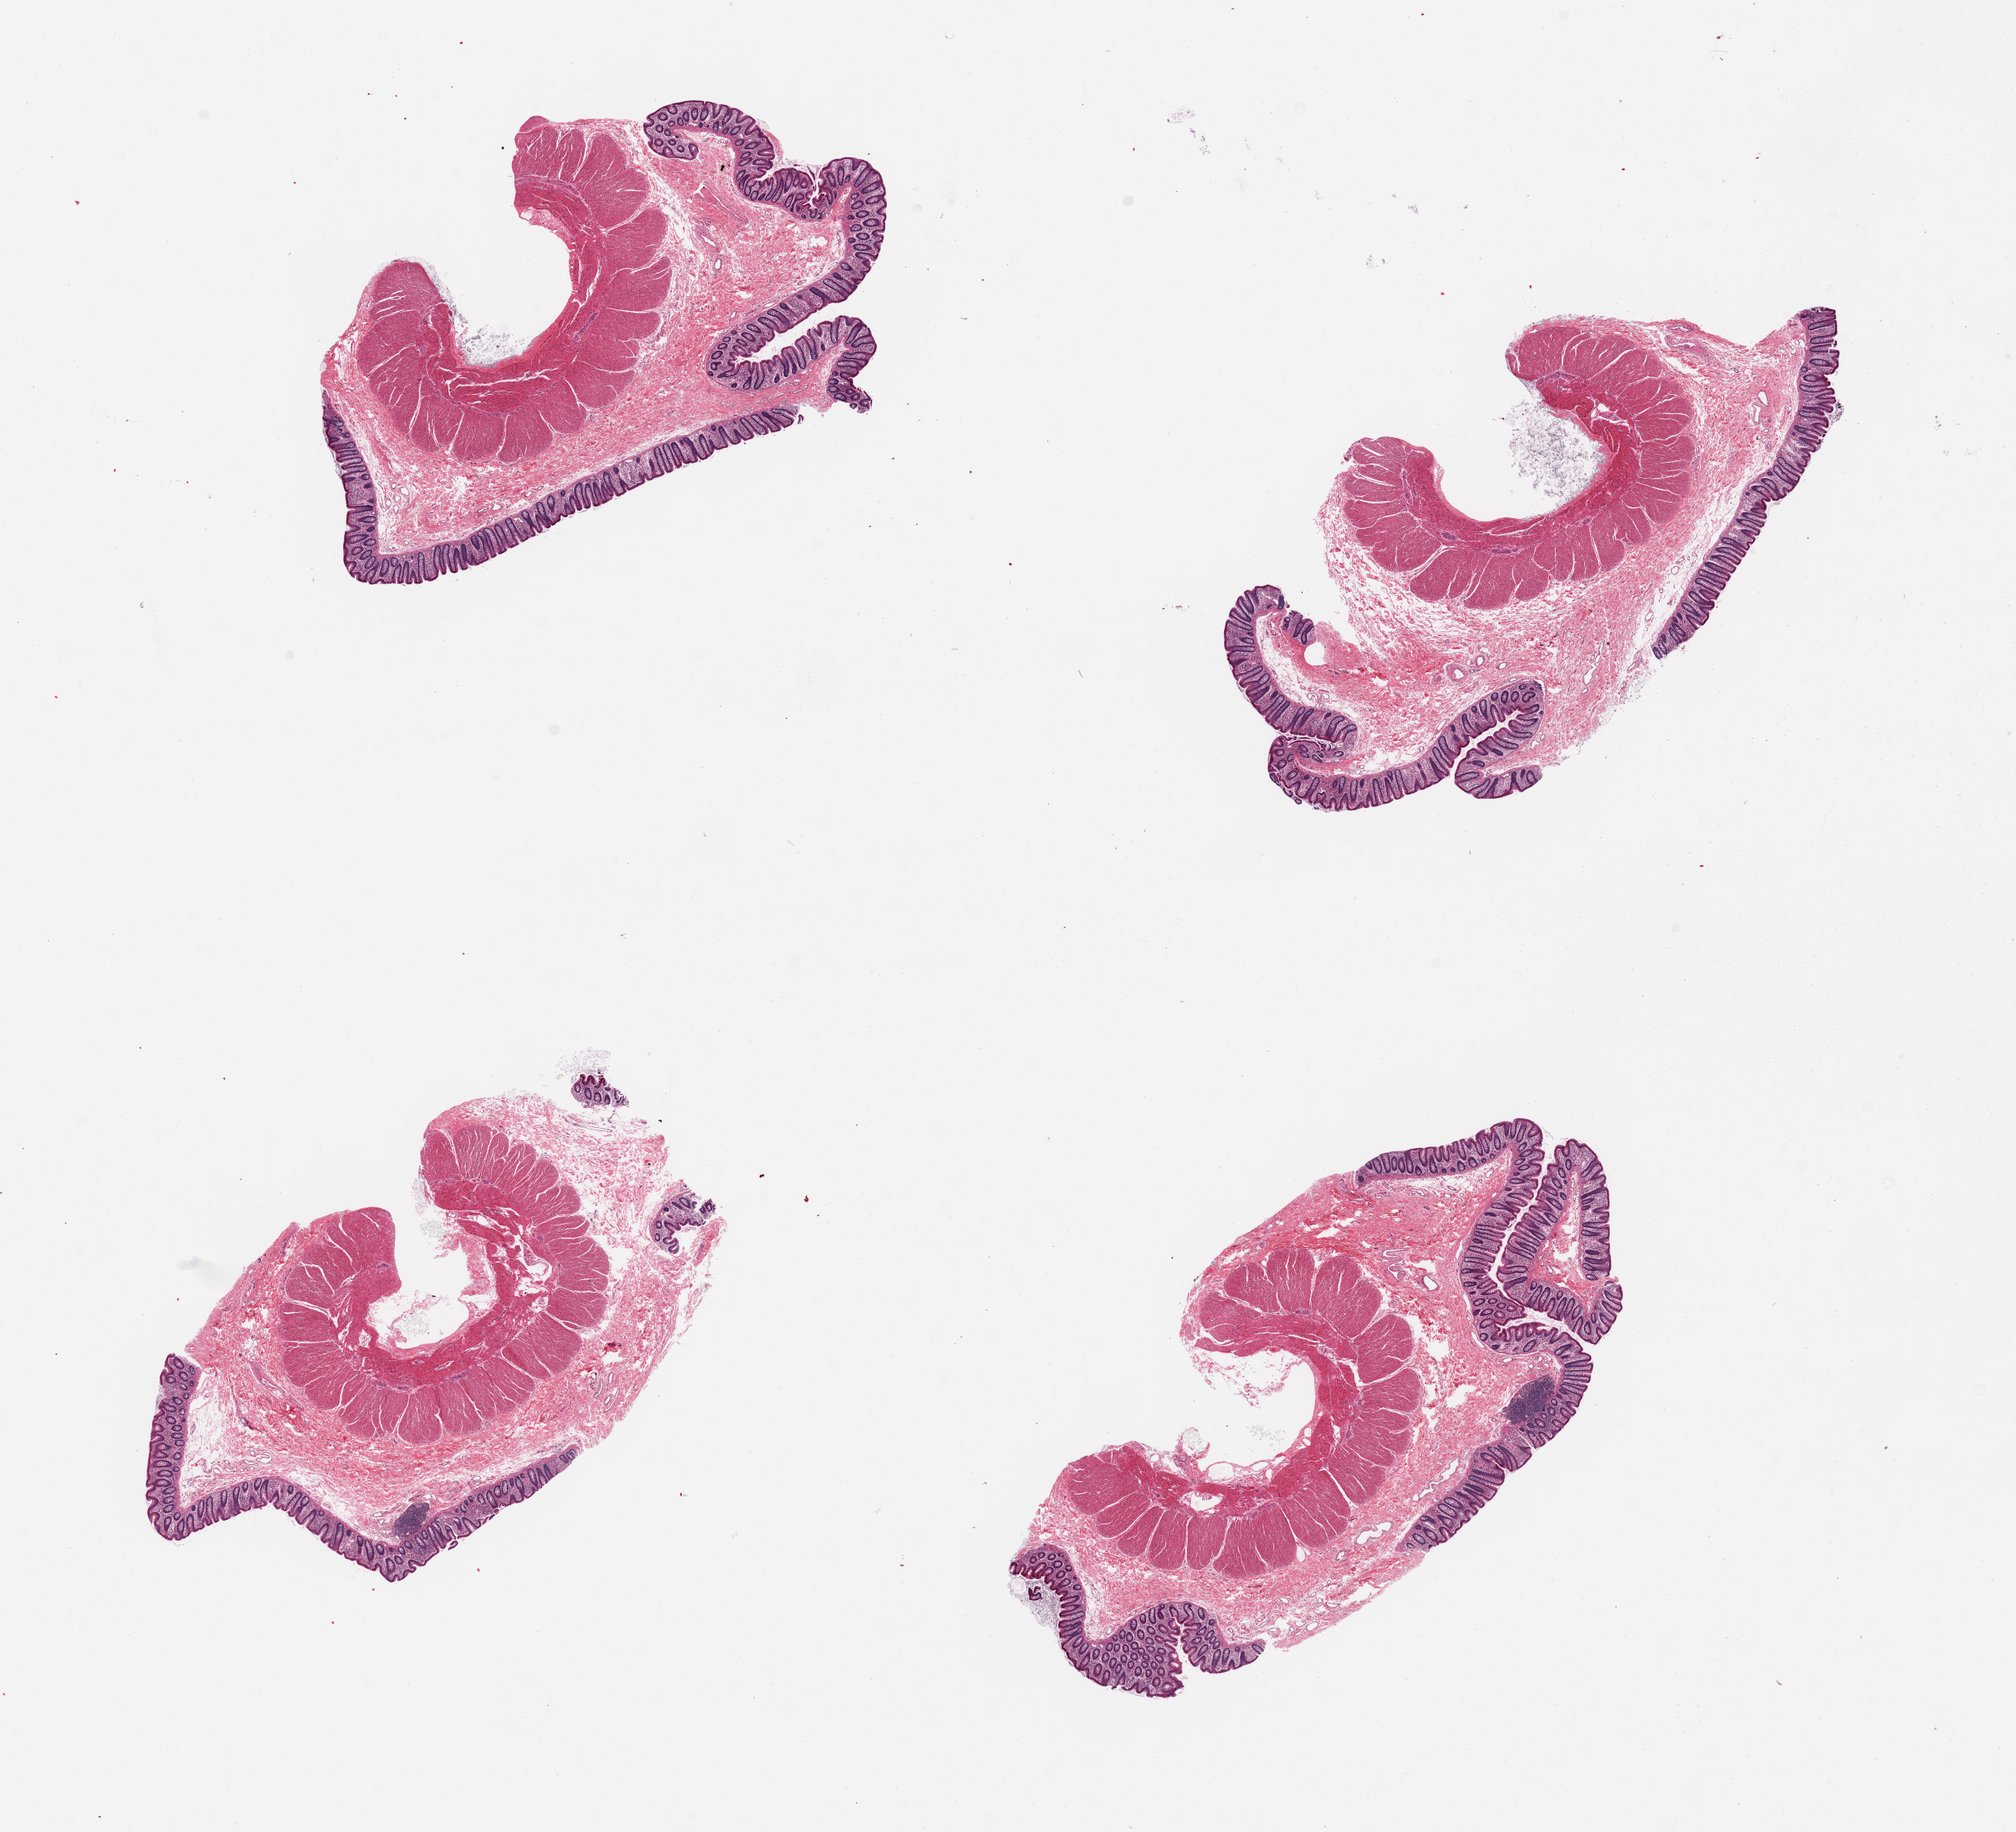
Digitized H&E-stained section, brightfield — a low-resolution overview of the entire scanned area, about 20.7 x 18.8 mm (slide scanned at 20x). PAXgene-fixed paraffin-embedded (PFPE) section. Sampled site (target tissue): transverse colon. Donor tissue sample. Female donor.
Reviewer comment on this tissue sample: 4 pieces.